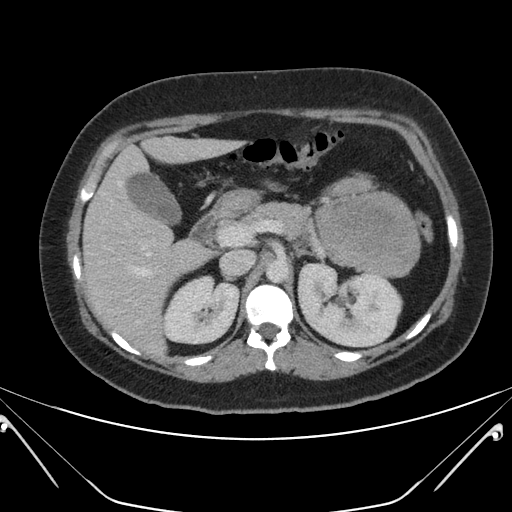
Contrast-enhanced abdominal CT, one axial slice. Position 125 of 168 along the scan axis. Soft-tissue window (W 400 / L 40 HU). 3 mm slice thickness. 512 × 512 image matrix, field of view 394 × 394 mm. Patient: female, 26 years. From the clinical record (not read from this slice): diagnosis: adrenocortical carcinoma; tumour side: left adrenal; tumour size at pathology: 28 cm; Ki-67 index: 20 %; stage (as recorded): 2.
Annotated regions visible in this slice (semi-automatically segmented with operator editing):
- mass: bounding box (x1, y1, x2, y2) in pixels: (317, 180, 418, 276)